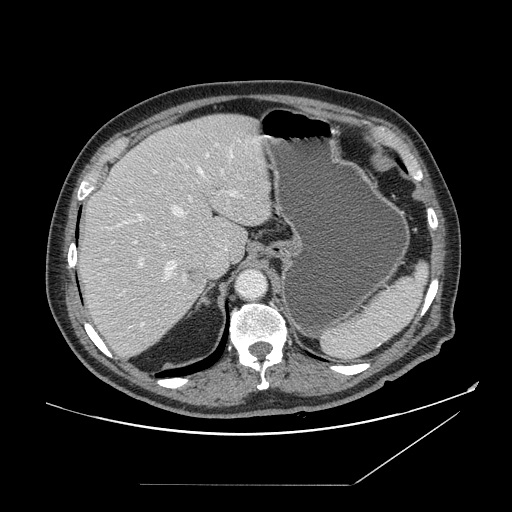
Contrast-enhanced abdominal CT, one axial slice; slice 114 of 166 in the series (ordered by position); intravenous contrast given; soft-tissue window (W 400 / L 40 HU); 2.5 mm slice thickness; 512 × 512 image matrix, field of view 416 × 416 mm. Male patient, age 80 years. Case-level facts recorded for this patient, not image findings: diagnosis: colorectal cancer liver metastases, imaged before liver resection.
Structures marked on this image (outlined manually by an expert reader):
- hepatic veins: bounding box <120,153,233,280> (left, top, right, bottom; pixels)
- liver: <78,114,272,358>
- planned liver remnant (the part of the liver to remain after resection): <84,114,271,262>
- portal vein (with intrahepatic branches): <136,154,237,325>
- liver metastasis: <189,271,195,275>
- liver metastasis: <186,270,197,281>